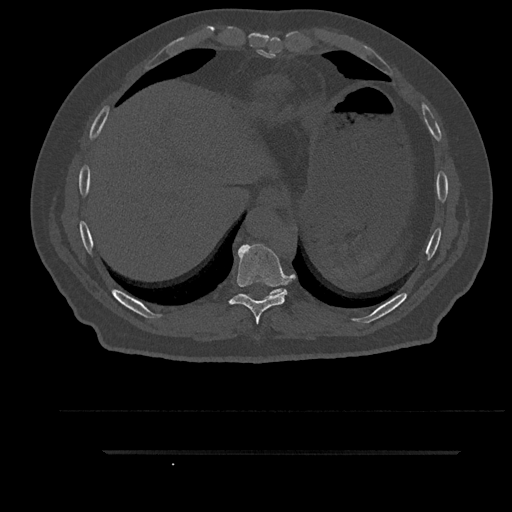
CT including the spine, one axial slice; position 417 of 797 along the scan axis; reconstruction kernel Br40s/3; 120 kVp; bone window (W 1800 / L 400 HU); 0.5 mm slice thickness; 512 × 512 image matrix. Male patient, age 63 years. Case-level facts recorded for this patient, not image findings: primary cancer: renal.
Outlined on this slice (semi-automatic segmentation, software-assisted and operator-edited):
- T10 vertebra: bounding box <244,289,285,296> (left, top, right, bottom; pixels)
- T9 vertebra: <229,244,291,324>